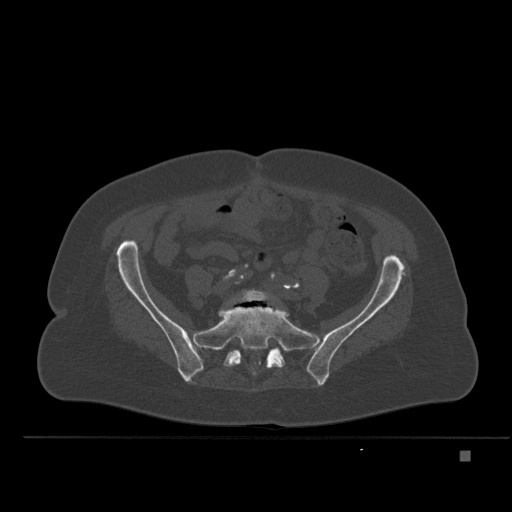
CT including the spine, one axial slice. Slice 146 of 477 in the series (ordered by position). Bone window (W 1800 / L 400 HU). 1.5 mm slice thickness. 512 × 512 image matrix. Patient: female, 74 years. Case-level facts recorded for this patient, not image findings: primary cancer: colon.
Annotated regions visible in this slice (semi-automatic segmentation, software-assisted and operator-edited):
- L5 vertebra: bounding box (x1, y1, x2, y2) in pixels: (239, 289, 269, 302)